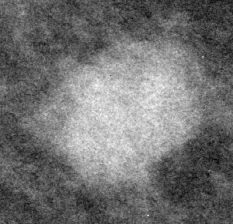
Cropped region of a digitized screen-film mammogram centred on a radiologist-marked abnormality, left breast, MLO view, BI-RADS breast density category 1 (scale 1–4).
Marked abnormality: mass, shape lobulated, margins ill defined; BI-RADS assessment category 4; subtlety rating 4 on a 1 (subtle) to 5 (obvious) scale; pathology (as recorded): malignant.